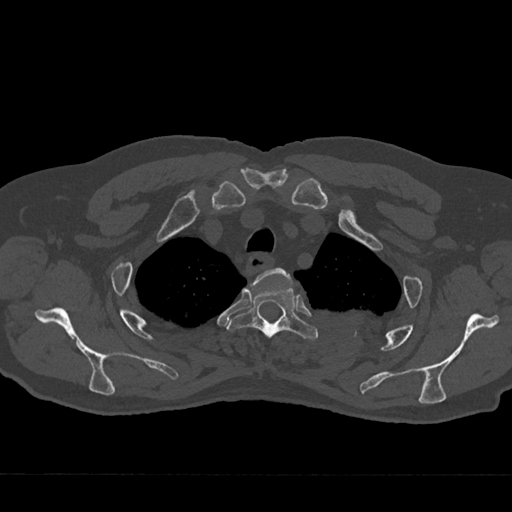
CT including the spine, one axial slice. Position 577 of 797 along the scan axis. 120 kVp. Bone window (W 1800 / L 400 HU). 0.5 mm slice thickness. 512 × 512 image matrix, field of view 377 × 377 mm. Patient: male, 75 years. From the clinical record (not read from this slice): primary cancer: renal; vertebrae with lytic lesions (as recorded): T4.
Structures marked on this image (semi-automatically segmented with operator editing):
- T2 vertebra: box from (x=251, y=268) to (x=291, y=286) px
- T3 vertebra: (x=229, y=283)–(x=317, y=340)